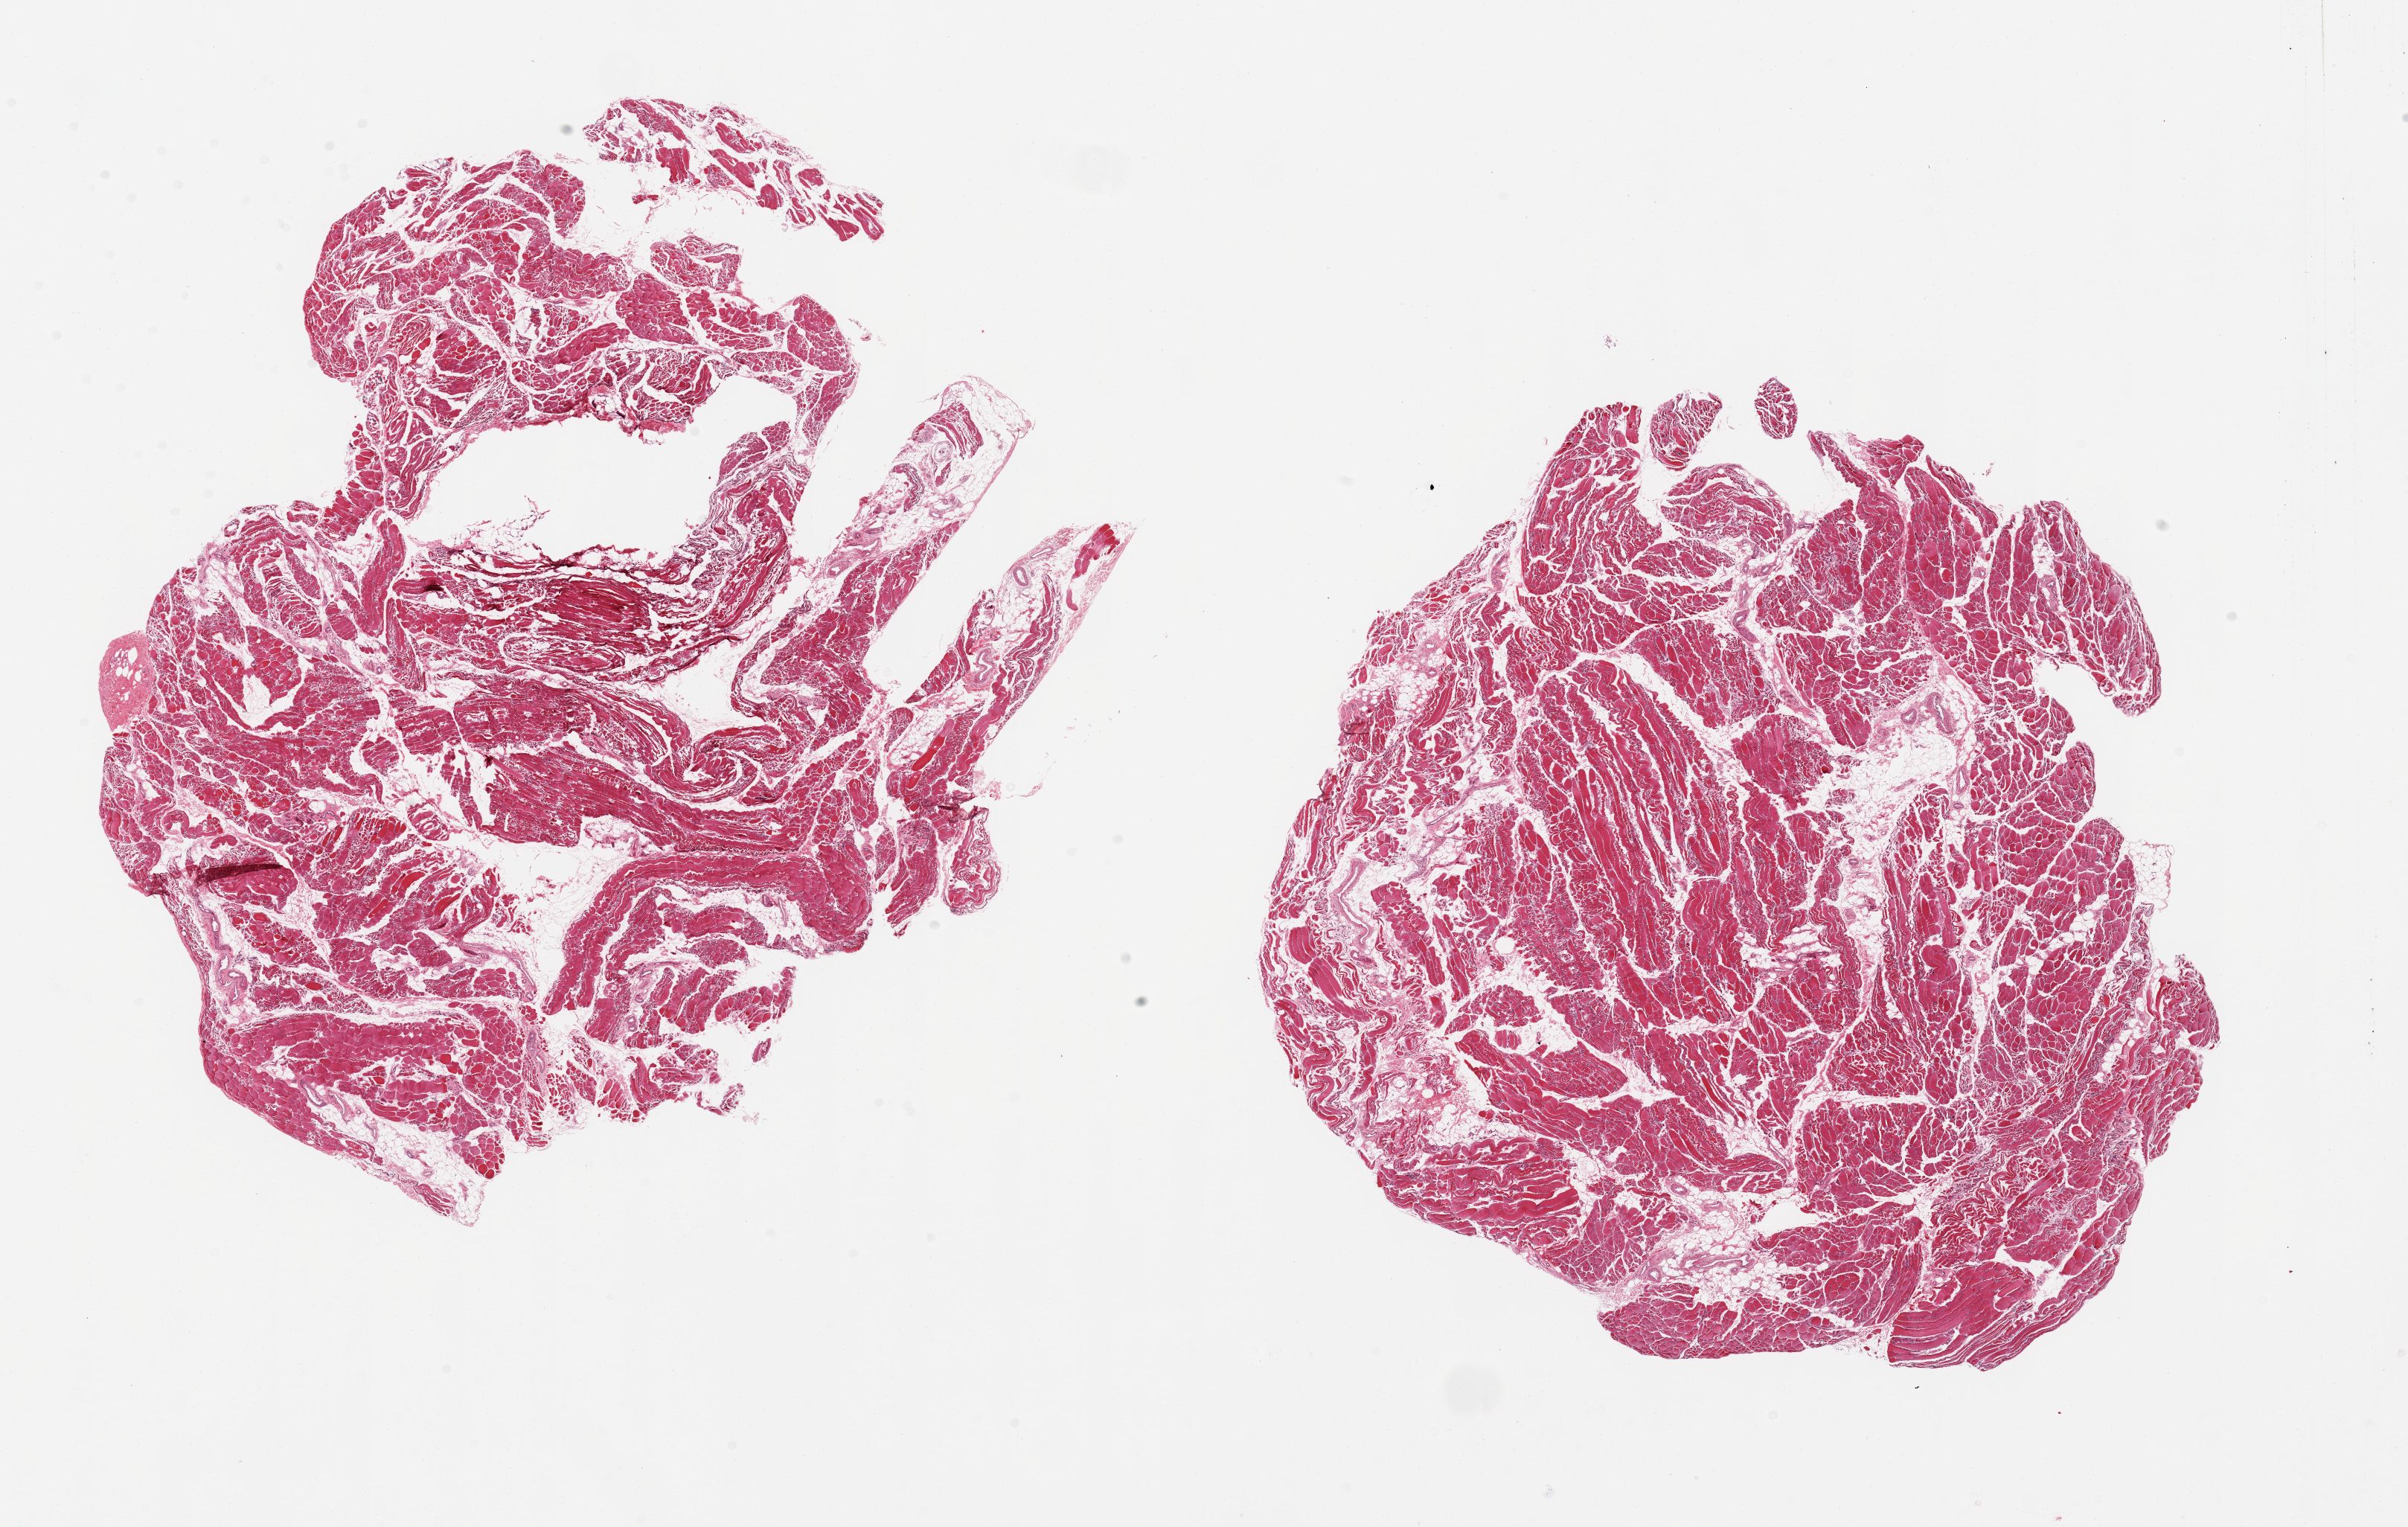
Haematoxylin and eosin whole-slide image — a low-resolution overview of the entire scanned area, about 25.6 x 16.2 mm (slide scanned at 20x); PAXgene-fixed, paraffin-embedded tissue; target tissue: skeletal muscle; donor tissue sample. Donor: male.
Reviewer comment on this tissue sample: 2 pieces, atrophic muscle fibers; interstitial fat/connective tissue is ~40%.